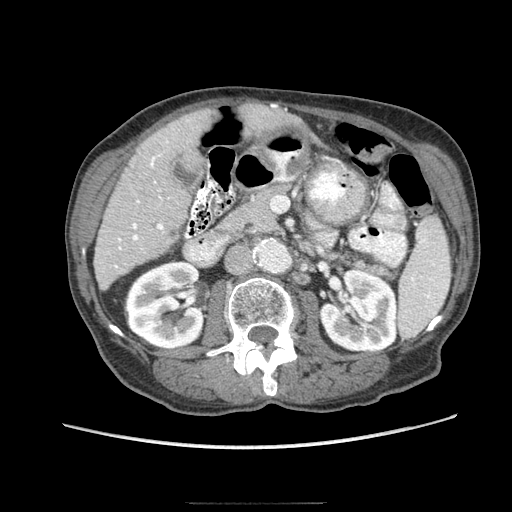
Contrast-enhanced abdominal CT (liver protocol), one axial slice. Slice 32 of 83 in the series (ordered by position). Soft-tissue window (W 400 / L 40 HU). 512 × 512 image matrix, field of view 360 × 360 mm. From the clinical record (not read from this slice): diagnosis: hepatocellular carcinoma (patient treated with transarterial chemoembolisation; whether this scan precedes or follows treatment is not stated here); TNM stage (as recorded): Stage-I; Child-Pugh class: A; tumour differentiation: moderately differentiated.
Structures marked on this image (semi-automatic segmentation, software-assisted and operator-edited):
- liver parenchyma outside the tumour (the mass and vessels are separate outlines, so this box may not span the whole liver): bounding box (x1, y1, x2, y2) in pixels: (94, 102, 292, 290)
- liver vessels: (115, 104, 276, 268)